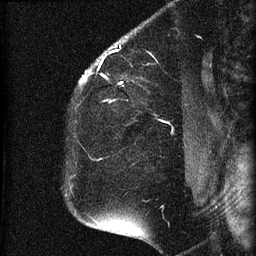
Breast MRI (dynamic contrast-enhanced), one sagittal slice; position 51 of 60 along the scan axis; dynamic contrast-enhanced series, image 2 of 4 at this slice position (ordered by acquisition); 1.5 T; TE 4.2 ms, TR 22.7 ms; 1.5 mm slice thickness; 256 × 256 image matrix, field of view 180 × 180 mm. Patient: female, 35 years. From the clinical record (not read from this slice): setting: breast cancer imaged before/during neoadjuvant chemotherapy; receptor status: HR-positive, HER2-negative.
Annotated regions visible in this slice (semi-automatically segmented with operator editing):
- analysis volume of interest (the breast-tissue region the enhancement analysis was run in; not a lesion): box from (x=69, y=27) to (x=199, y=112) px
- tumour enhancement mask (voxels above the 90 % enhancement threshold inside the analysis volume of interest): (x=79, y=49)–(x=121, y=103)